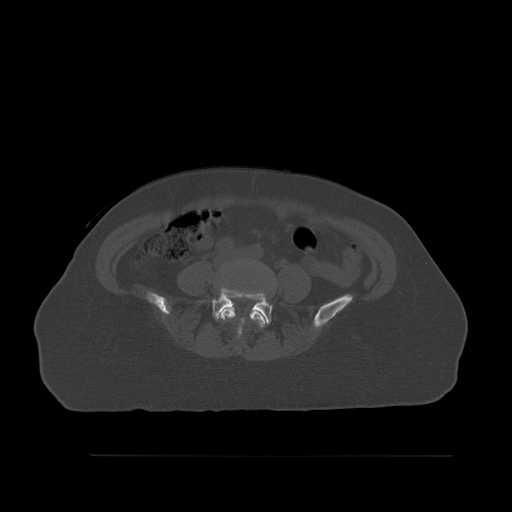
CT including the spine, one axial slice. Position 196 of 527 along the scan axis. Bone window (W 1800 / L 400 HU). 1.5 mm slice thickness. 512 × 512 image matrix. Female patient, age 73 years. Case-level facts recorded for this patient, not image findings: primary cancer: breast; vertebrae with lytic lesions (as recorded): L2.
Outlined on this slice (semi-automatically segmented with operator editing):
- L4 vertebra: bounding box (x1, y1, x2, y2) in pixels: (220, 261, 267, 340)
- L5 vertebra: (213, 288, 272, 325)